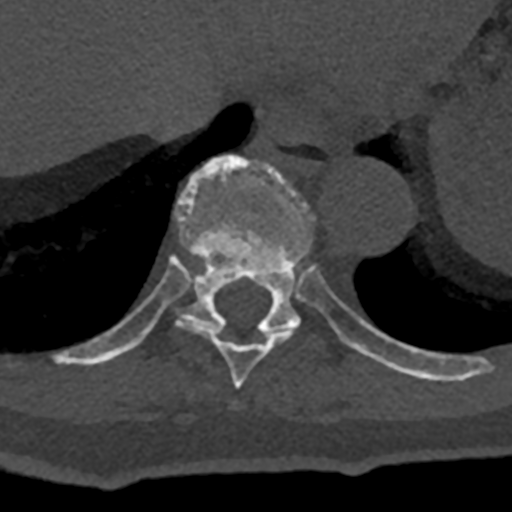
CT including the spine, one axial slice. Slice 627 of 797 in the series (ordered by position). 120 kVp. Bone window (W 1800 / L 400 HU). 0.5 mm slice thickness. 512 × 512 image matrix. Patient: male, 74 years. Case-level facts recorded for this patient, not image findings: primary cancer: renal; vertebrae with lytic lesions (as recorded): T10, L1, L2, L3, L4, L5.
Annotated regions visible in this slice (semi-automatic segmentation, software-assisted and operator-edited):
- T10 vertebra: box from (x=70, y=155) to (x=432, y=380) px
- T9 vertebra: (x=176, y=317)–(x=295, y=388)